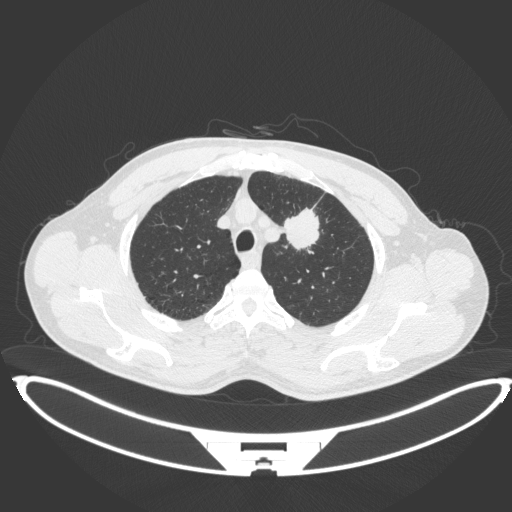
Chest CT, one axial slice; slice 356 of 407 in the series (ordered by position); 120 kVp; lung window (W 1500 / L -600 HU); 1 mm slice thickness; 512 × 512 image matrix, field of view 457 × 457 mm. Male patient, age 60 years. From the clinical record (not read from this slice): clinical TNM (as recorded): T2a N0 M0; histopathological grade: G1-G2.
Outlined on this slice (bounding box drawn by a radiologist):
- lung tumour (recorded histology: squamous cell carcinoma): box from (x=285, y=204) to (x=321, y=252) px